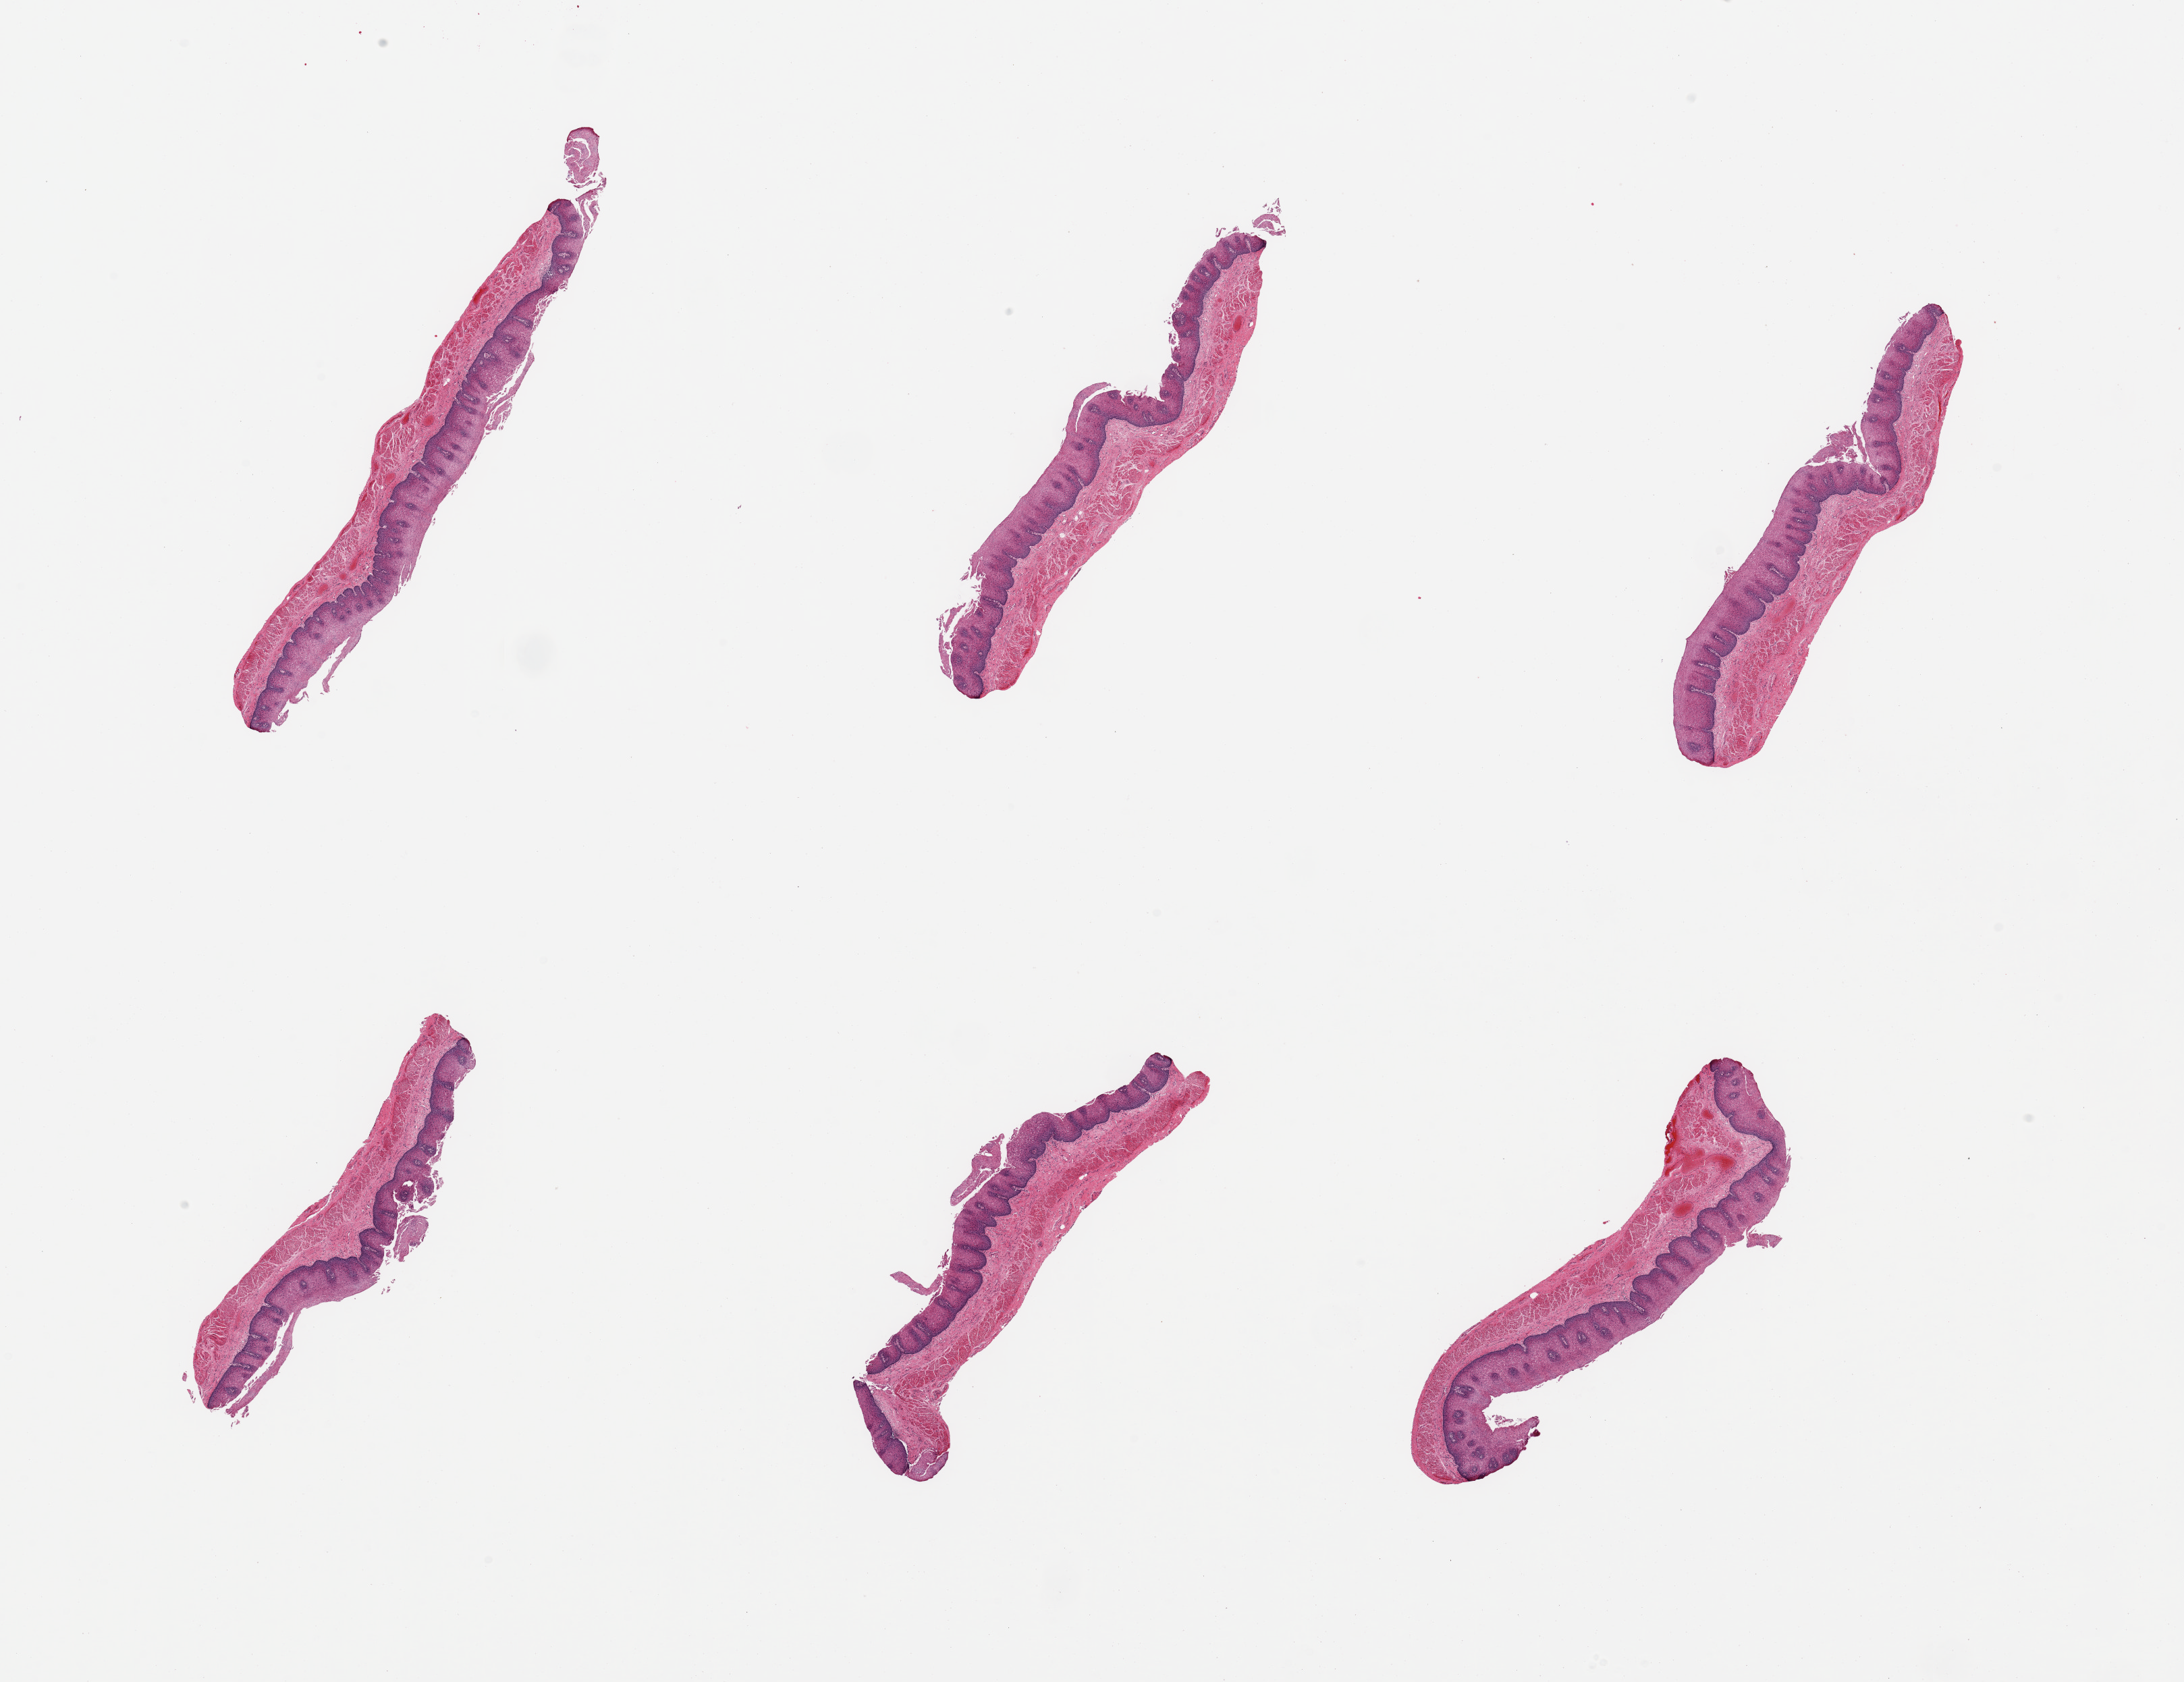
Whole-slide image, hematoxylin and eosin (H&E) stain, brightfield, low-resolution overview of the scanned area, about 25.6 x 19.7 mm. PAXgene-fixed paraffin-embedded (PFPE) section. Sampled site (target tissue): esophageal mucous membrane. Tissue donor sample. Donor: male.
Review note (as recorded): 6 pieces; 0.5mm thick stratified squamous epithelium and muscularis mucosae, congestion.